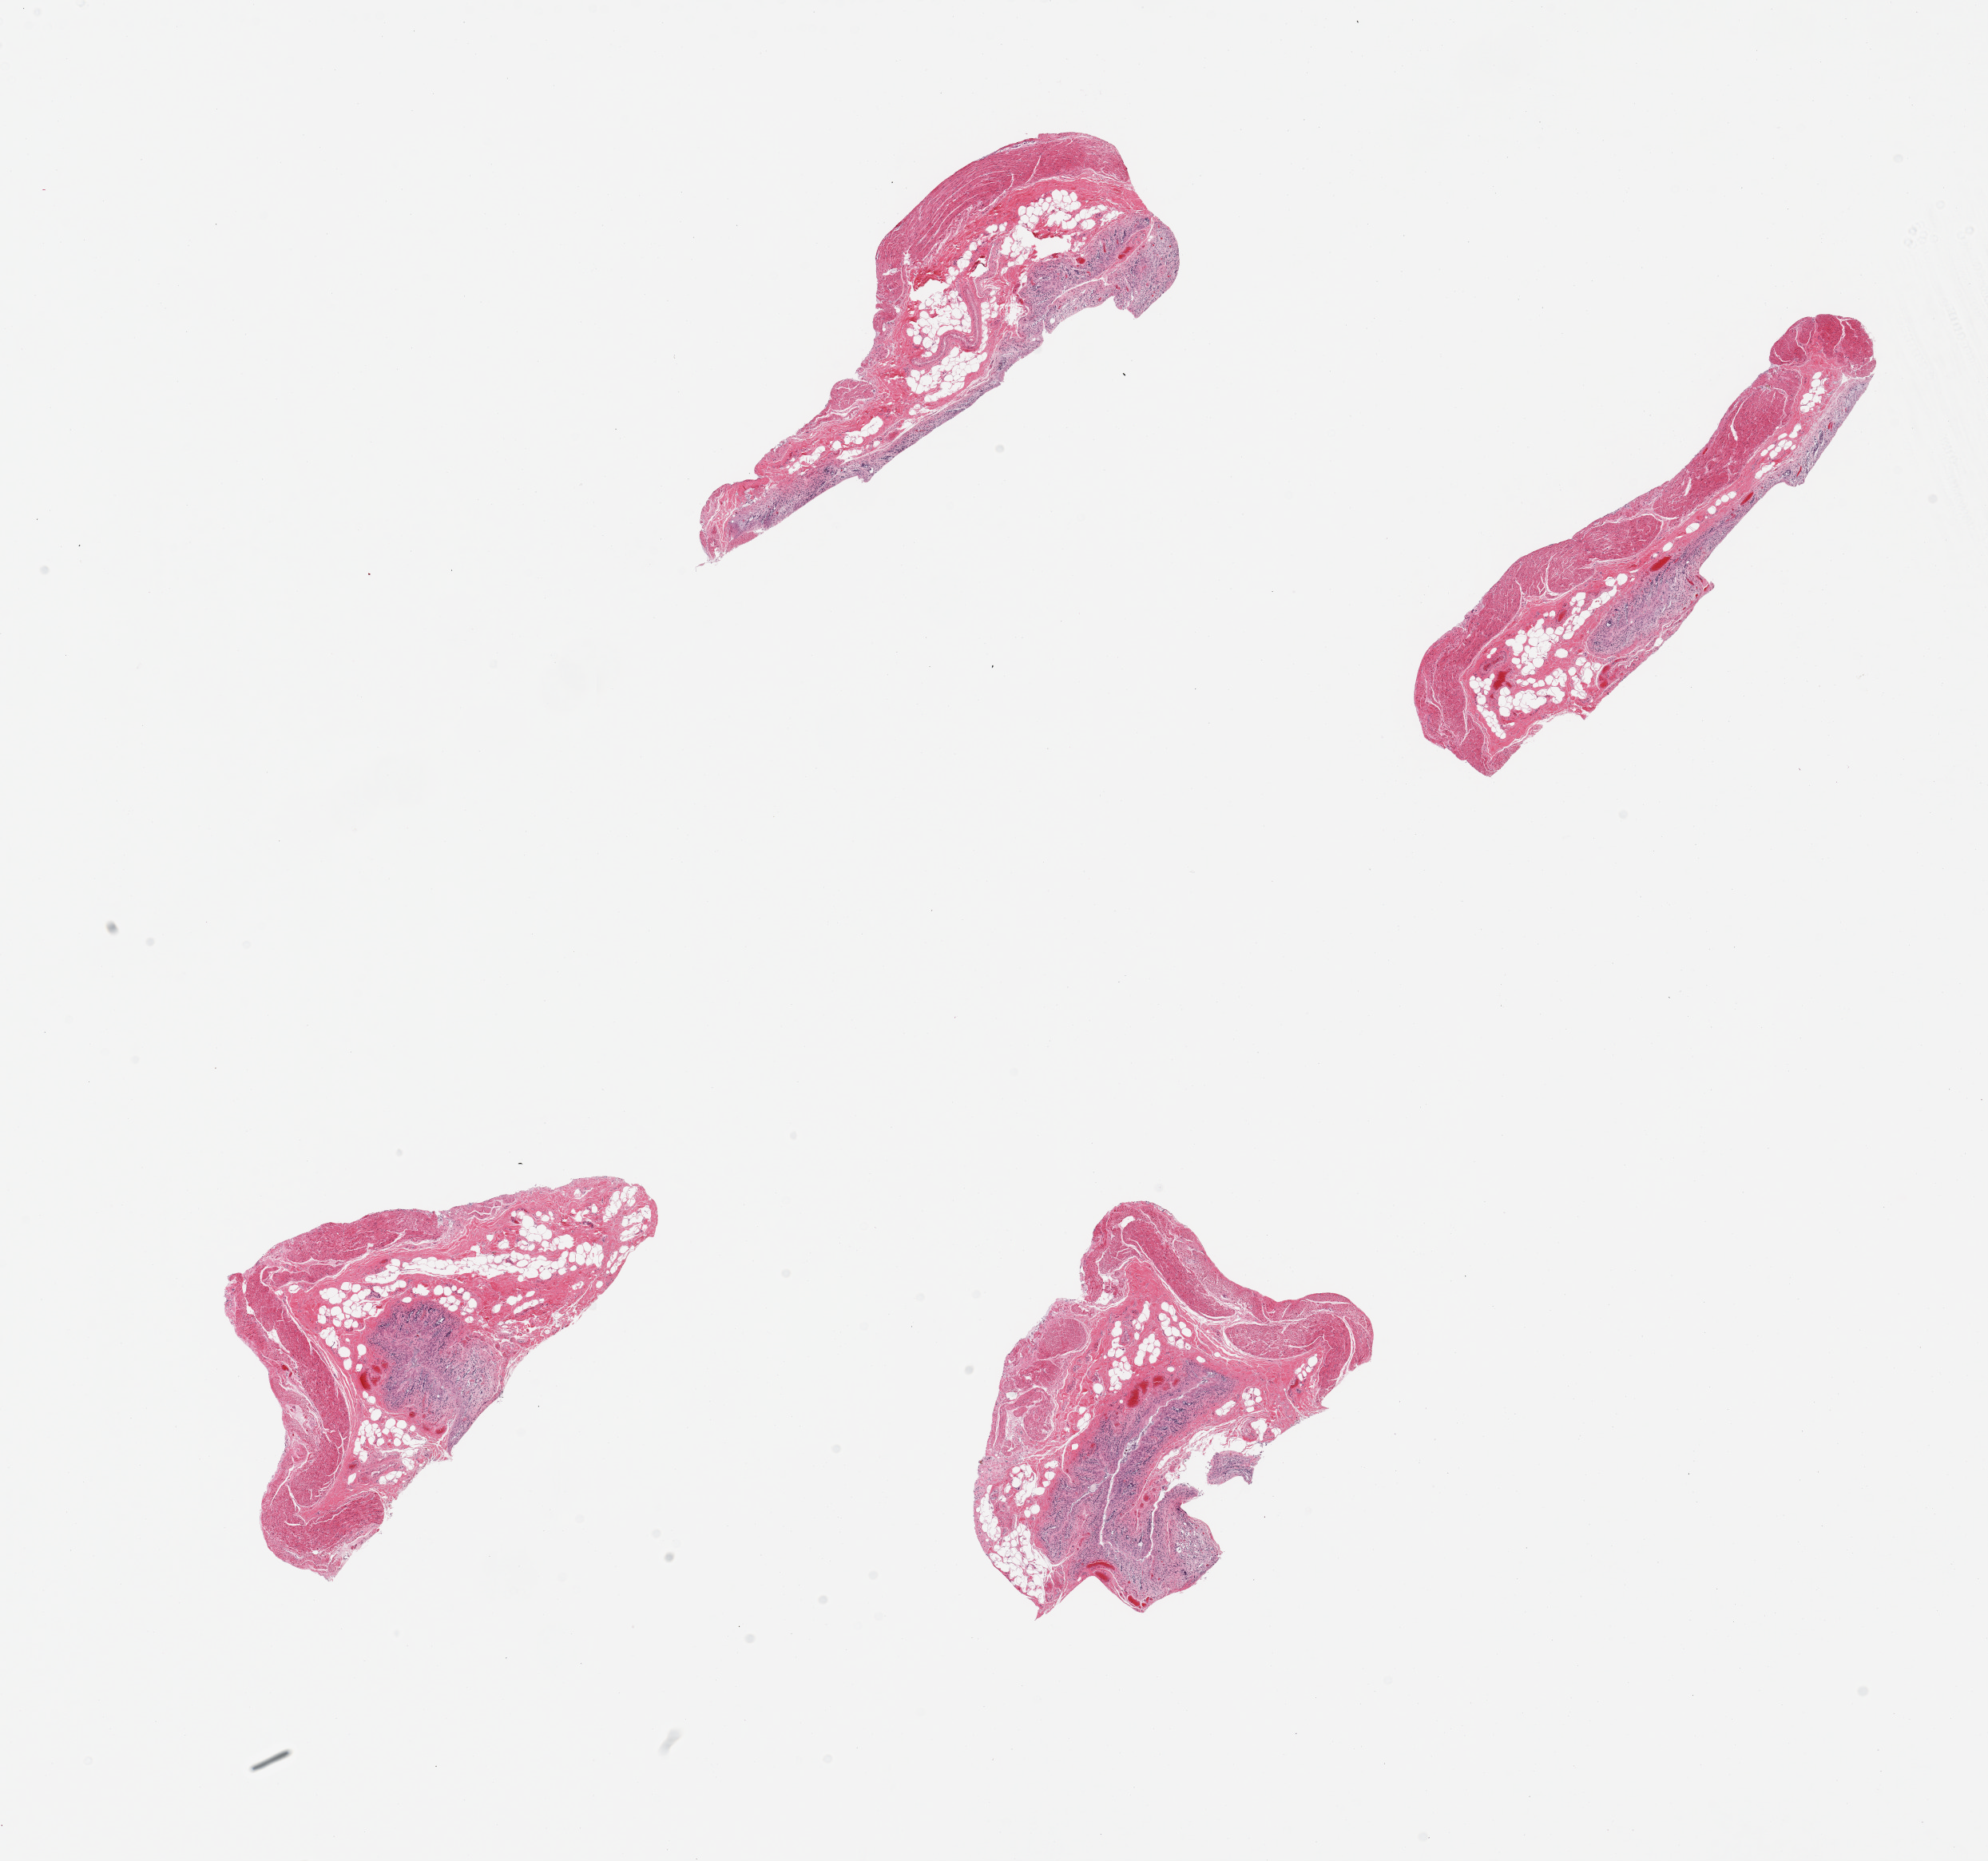
Digitized haematoxylin and eosin-stained section — a low-resolution overview of the entire scanned area, about 19.7 x 18.4 mm.
Specimen: PAXgene-fixed, paraffin-embedded tissue; section of transverse colon (target tissue); donor tissue sample.